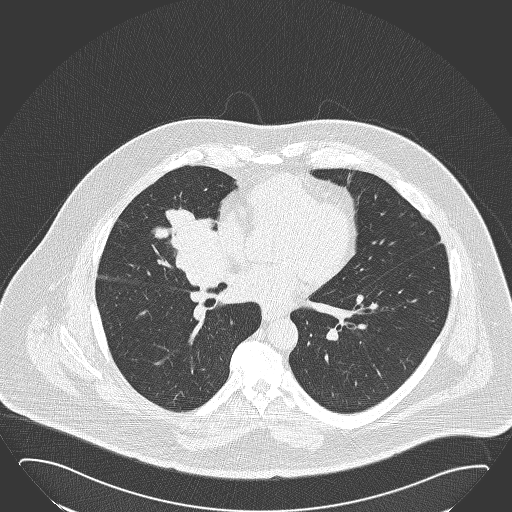
Low-dose screening chest CT, axial slice. Baseline screening round. Lung window (W 1500 / L -600 HU). 2 mm slice thickness. Slice 93 of 168 in the series. 512 × 512 image matrix. Male, age 61 years at enrolment. Former smoker at enrolment.
- Expert reader's lesion annotation, box from (x=143, y=196) to (x=230, y=283) px.
- The screening reader recorded 2 non-calcified nodules or masses ≥4 mm on this exam (right middle lobe, left lower lobe); which of them this box marks is not recorded.
- Official screen result: positive, change unspecified: nodule(s) >= 4 mm or enlarging nodule(s), mass(es), or other non-specific abnormalities suspicious for lung cancer.